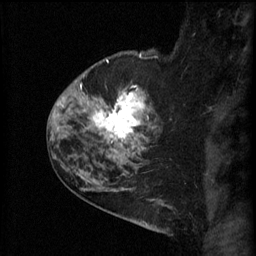
Breast MRI (dynamic contrast-enhanced), one sagittal slice; slice 45 of 60 in the series (ordered by position); 3 images stored at this slice position (order not interpretable as contrast timing); 1.5 T; TE 4.2 ms, TR 11 ms; 2.3 mm slice thickness; 256 × 256 image matrix, field of view 180 × 180 mm. Patient: female, 52 years.
Outlined on this slice (semi-automatically segmented with operator editing):
- analysis volume of interest (the breast-tissue region the enhancement analysis was run in; not a lesion): bounding box (x1, y1, x2, y2) in pixels: (86, 76, 163, 157)
- tumour enhancement mask (voxels above the 70 % enhancement threshold inside the analysis volume of interest): (92, 86, 149, 157)